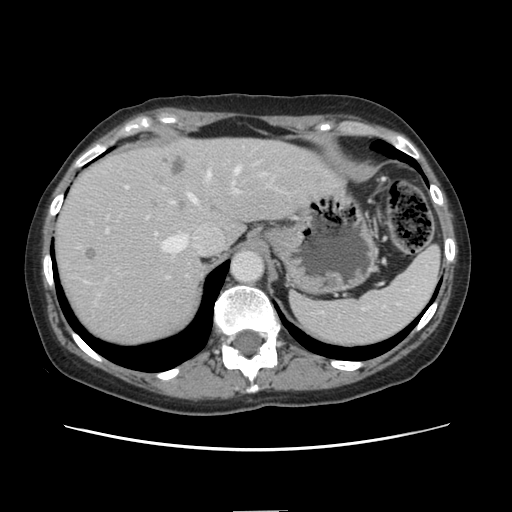
Contrast-enhanced abdominal CT, one axial slice; slice 110 of 141 in the series (ordered by position); 120 kVp; intravenous contrast given; soft-tissue window (W 400 / L 40 HU); 2.5 mm slice thickness; 512 × 512 image matrix, field of view 350 × 350 mm. Female patient, age 63 years. From the clinical record (not read from this slice): diagnosis: colorectal cancer liver metastases, imaged before liver resection; multiple liver metastases: yes; largest metastasis: 3.2 cm; disease in both lobes: yes.
Annotated regions visible in this slice (outlined manually by an expert reader):
- hepatic veins: box from (x=163, y=167) to (x=240, y=252) px
- liver: (x=54, y=138)–(x=336, y=347)
- planned liver remnant (the part of the liver to remain after resection): (x=191, y=139)–(x=338, y=242)
- portal vein (with intrahepatic branches): (x=207, y=179)–(x=239, y=192)
- liver metastasis: (x=153, y=173)–(x=166, y=186)